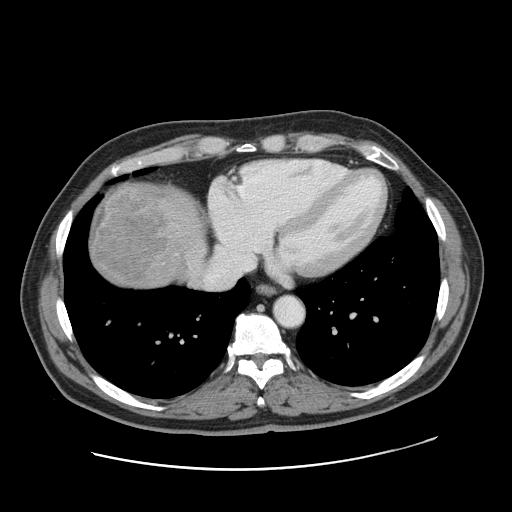
Contrast-enhanced abdominal CT, one axial slice; position 153 of 178 along the scan axis; intravenous contrast given; soft-tissue window (W 400 / L 40 HU); 2.5 mm slice thickness; 512 × 512 image matrix, field of view 403 × 403 mm. Male patient, age 63 years. Case-level facts recorded for this patient, not image findings: diagnosis: colorectal cancer liver metastases, imaged before liver resection; multiple liver metastases: yes.
Annotated regions visible in this slice (outlined manually by an expert reader):
- liver: bounding box <88,182,205,291> (left, top, right, bottom; pixels)
- liver metastasis: <92,185,164,280>